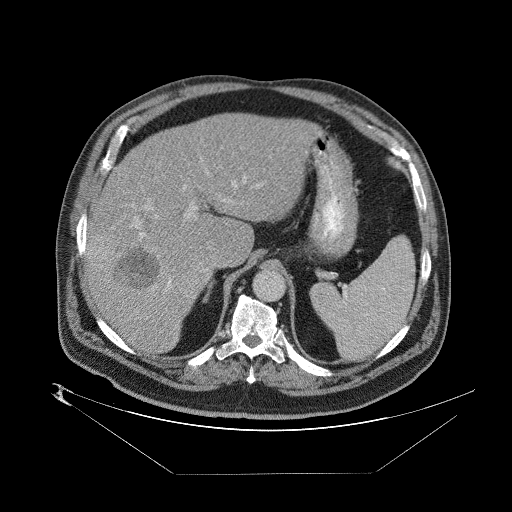
Contrast-enhanced abdominal CT (liver protocol), one axial slice; slice 56 of 89 in the series (ordered by position); 140 kVp; one of 2 acquisitions stored at this slice position; soft-tissue window (W 400 / L 40 HU); 512 × 512 image matrix, field of view 480 × 480 mm. Case-level facts recorded for this patient, not image findings: diagnosis: hepatocellular carcinoma (patient treated with transarterial chemoembolisation; whether this scan precedes or follows treatment is not stated here); TNM stage (as recorded): Stage-II; Child-Pugh class: B.
Annotated regions visible in this slice (semi-automatic segmentation, software-assisted and operator-edited):
- abdominal aorta: bounding box [x1, y1, x2, y2] px = [253, 267, 285, 300]
- liver parenchyma outside the tumour (the mass and vessels are separate outlines, so this box may not span the whole liver): [84, 110, 310, 352]
- mass: [90, 241, 215, 291]
- liver vessels: [109, 145, 272, 315]